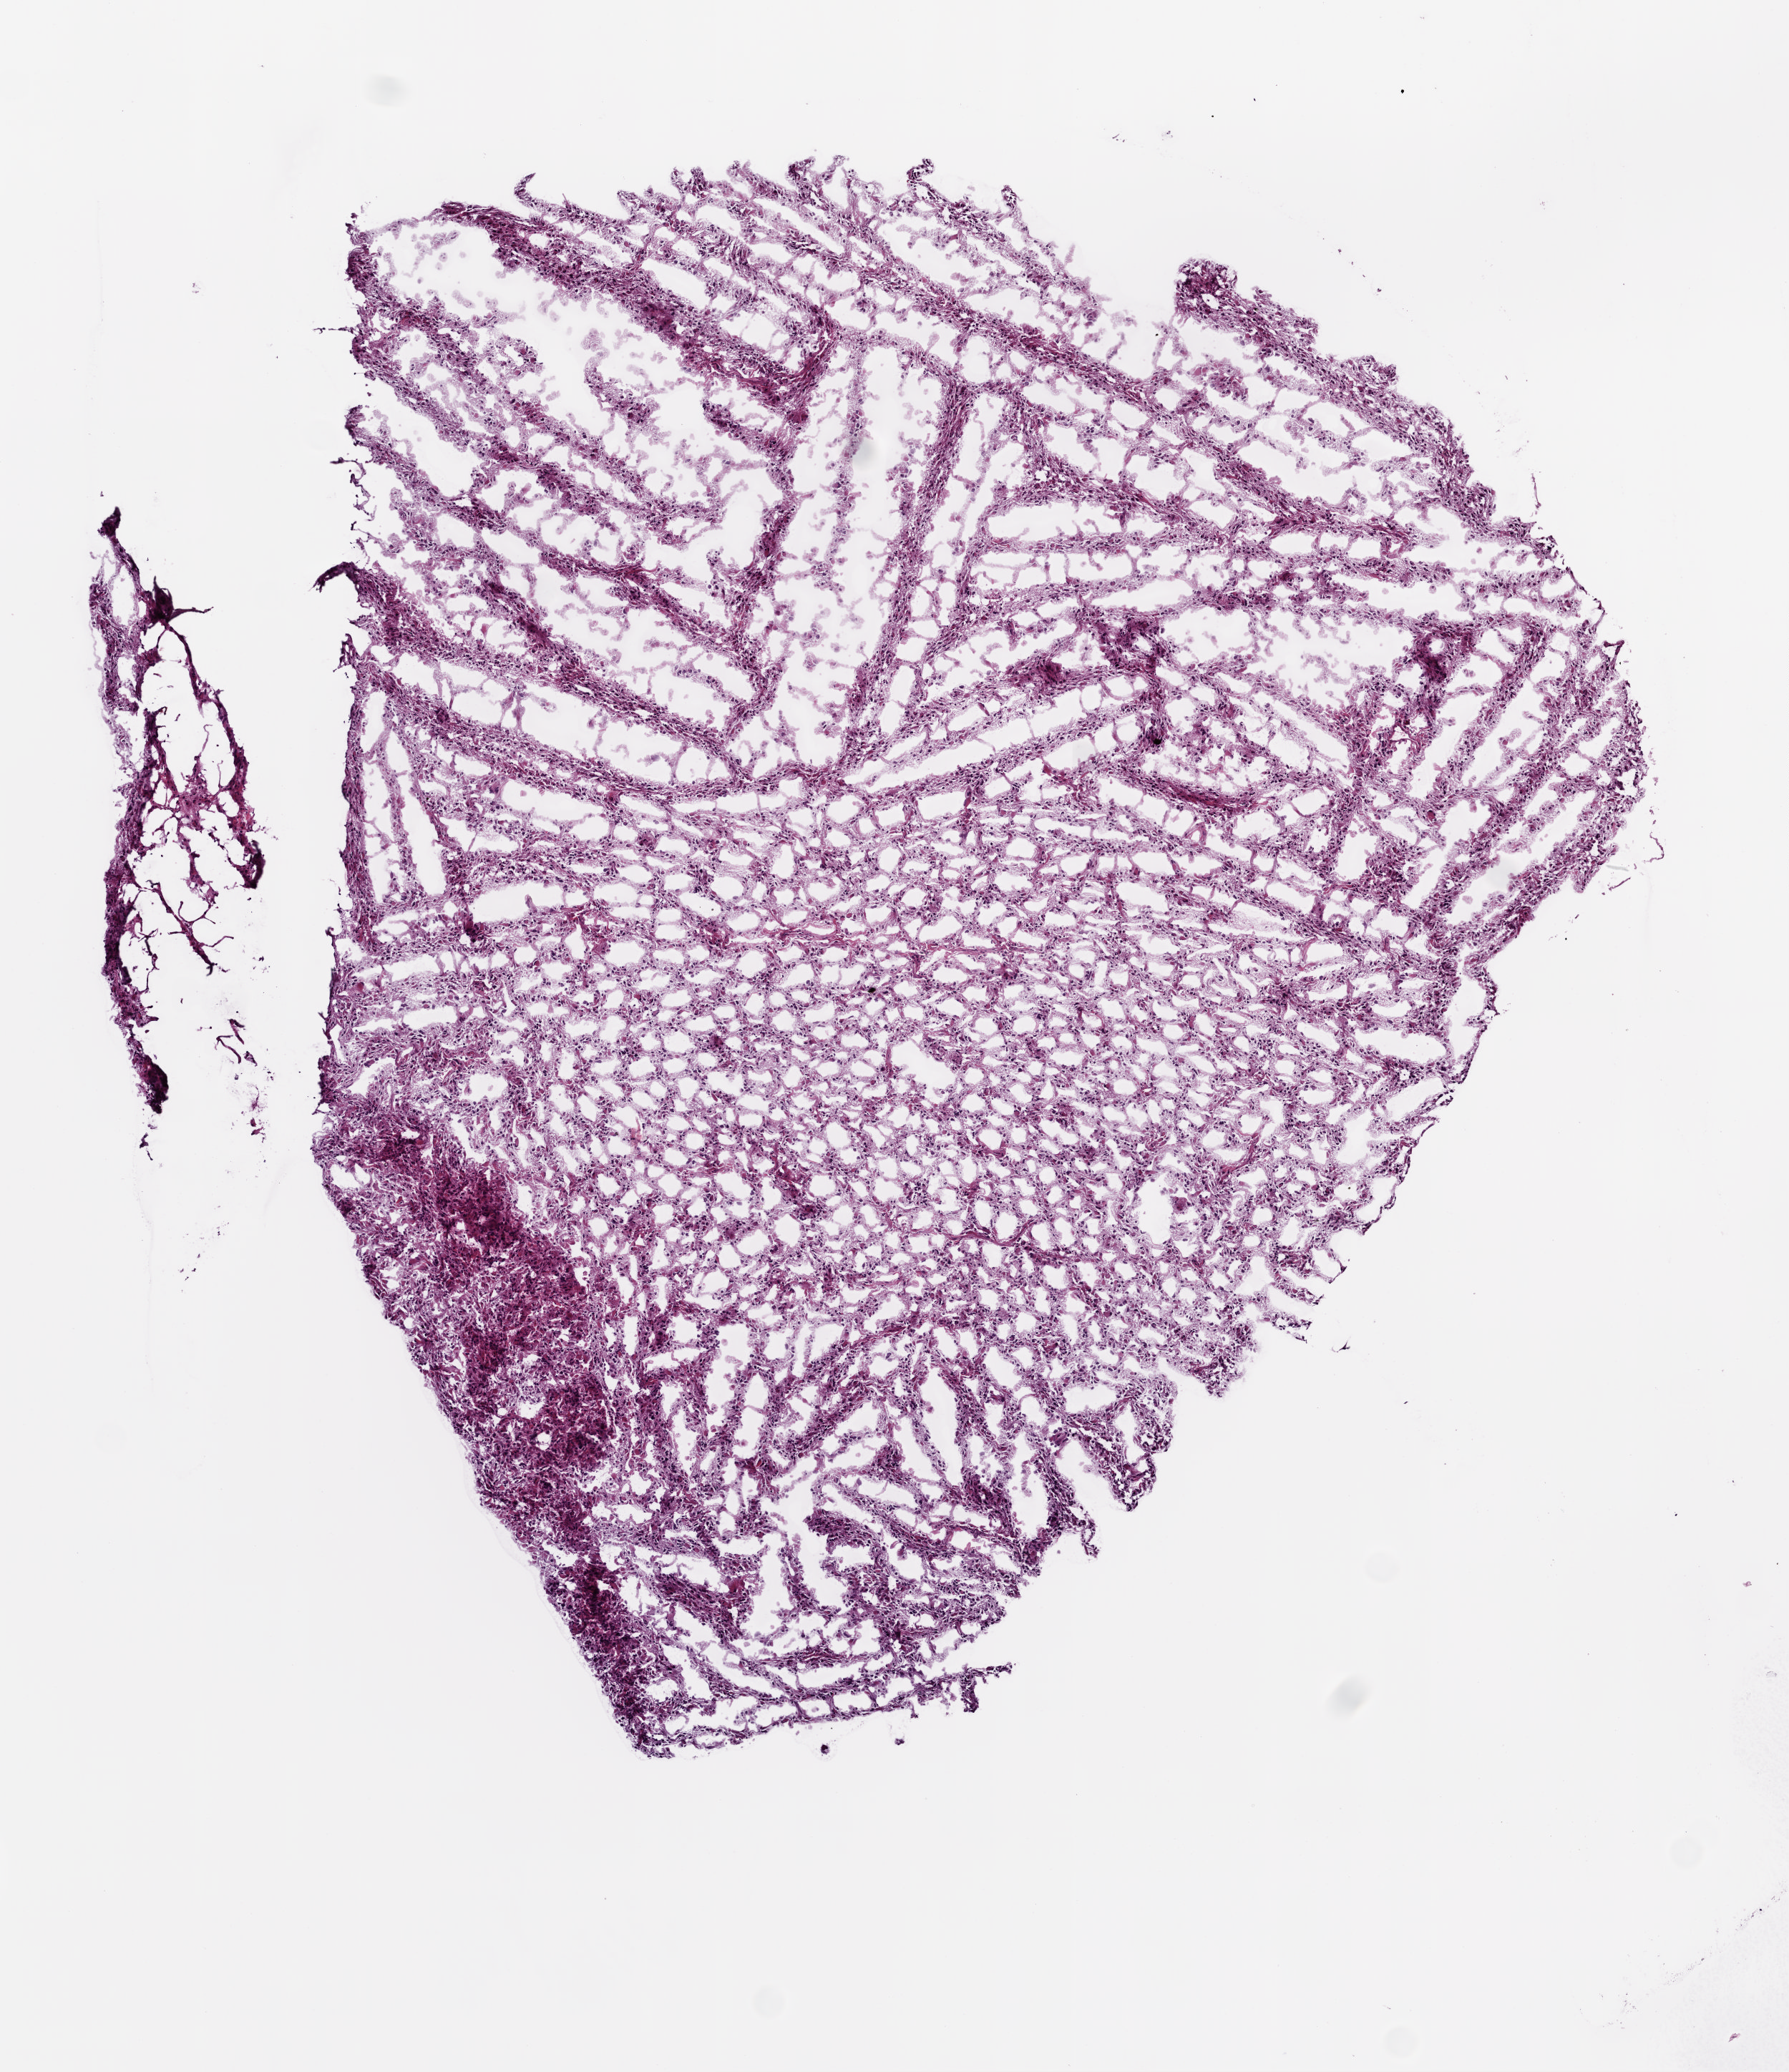
H&E-stained whole-slide image, shown as a low-resolution overview of the whole scanned area (about 5.0 x 5.8 mm, slide scanned at 20x). Frozen section from the bottom of the tissue portion. Brain, primary tumour sample. Patient: male, age at initial diagnosis 29 years. Histologic grade: G3 (poorly differentiated). Pathologist review of this section (percent, as recorded): tumour cells 100%, tumour nuclei 65%, normal cells 0%, stromal cells 0%, necrosis 0%.
* laterality: left
* diagnosis: Astrocytoma, anaplastic (cerebrum)